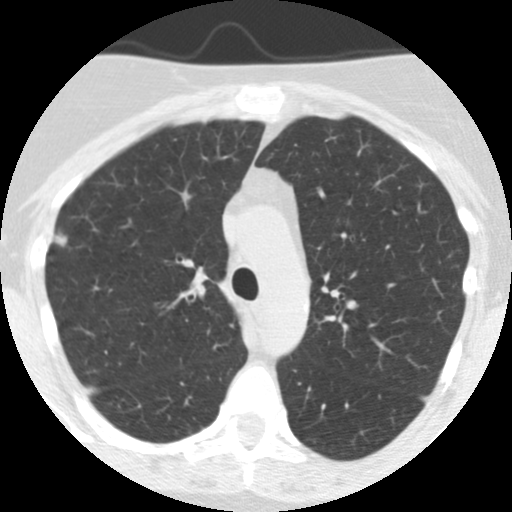
Chest CT (low-dose screening protocol), one axial image. Baseline annual screen. Lung window (W 1500 / L -600 HU). 2.5 mm slice thickness. Standard (soft-tissue) reconstruction kernel (STANDARD). Slice 173 of 249 in the series. Female participant, aged 55 years at enrolment. Current smoker at enrolment.
Expert reader's lesion annotation, bounding box (x1, y1, x2, y2) in pixels: (33, 219, 82, 269). Screening reader's record for this exam (one nodule recorded; not confirmed to be the boxed lesion): non-calcified nodule or mass ≥4 mm, right upper lobe, 7 × 7 mm, spiculated (stellate) margins, soft tissue attenuation. Later outcome: lung cancer diagnosed 1018 days after this screen (after the third annual screen) — bronchiolo-alveolar adenocarcinoma, NOS, right upper lobe, moderately differentiated (G2), stage IIA (AJCC 6th edition), 13 mm at pathology.